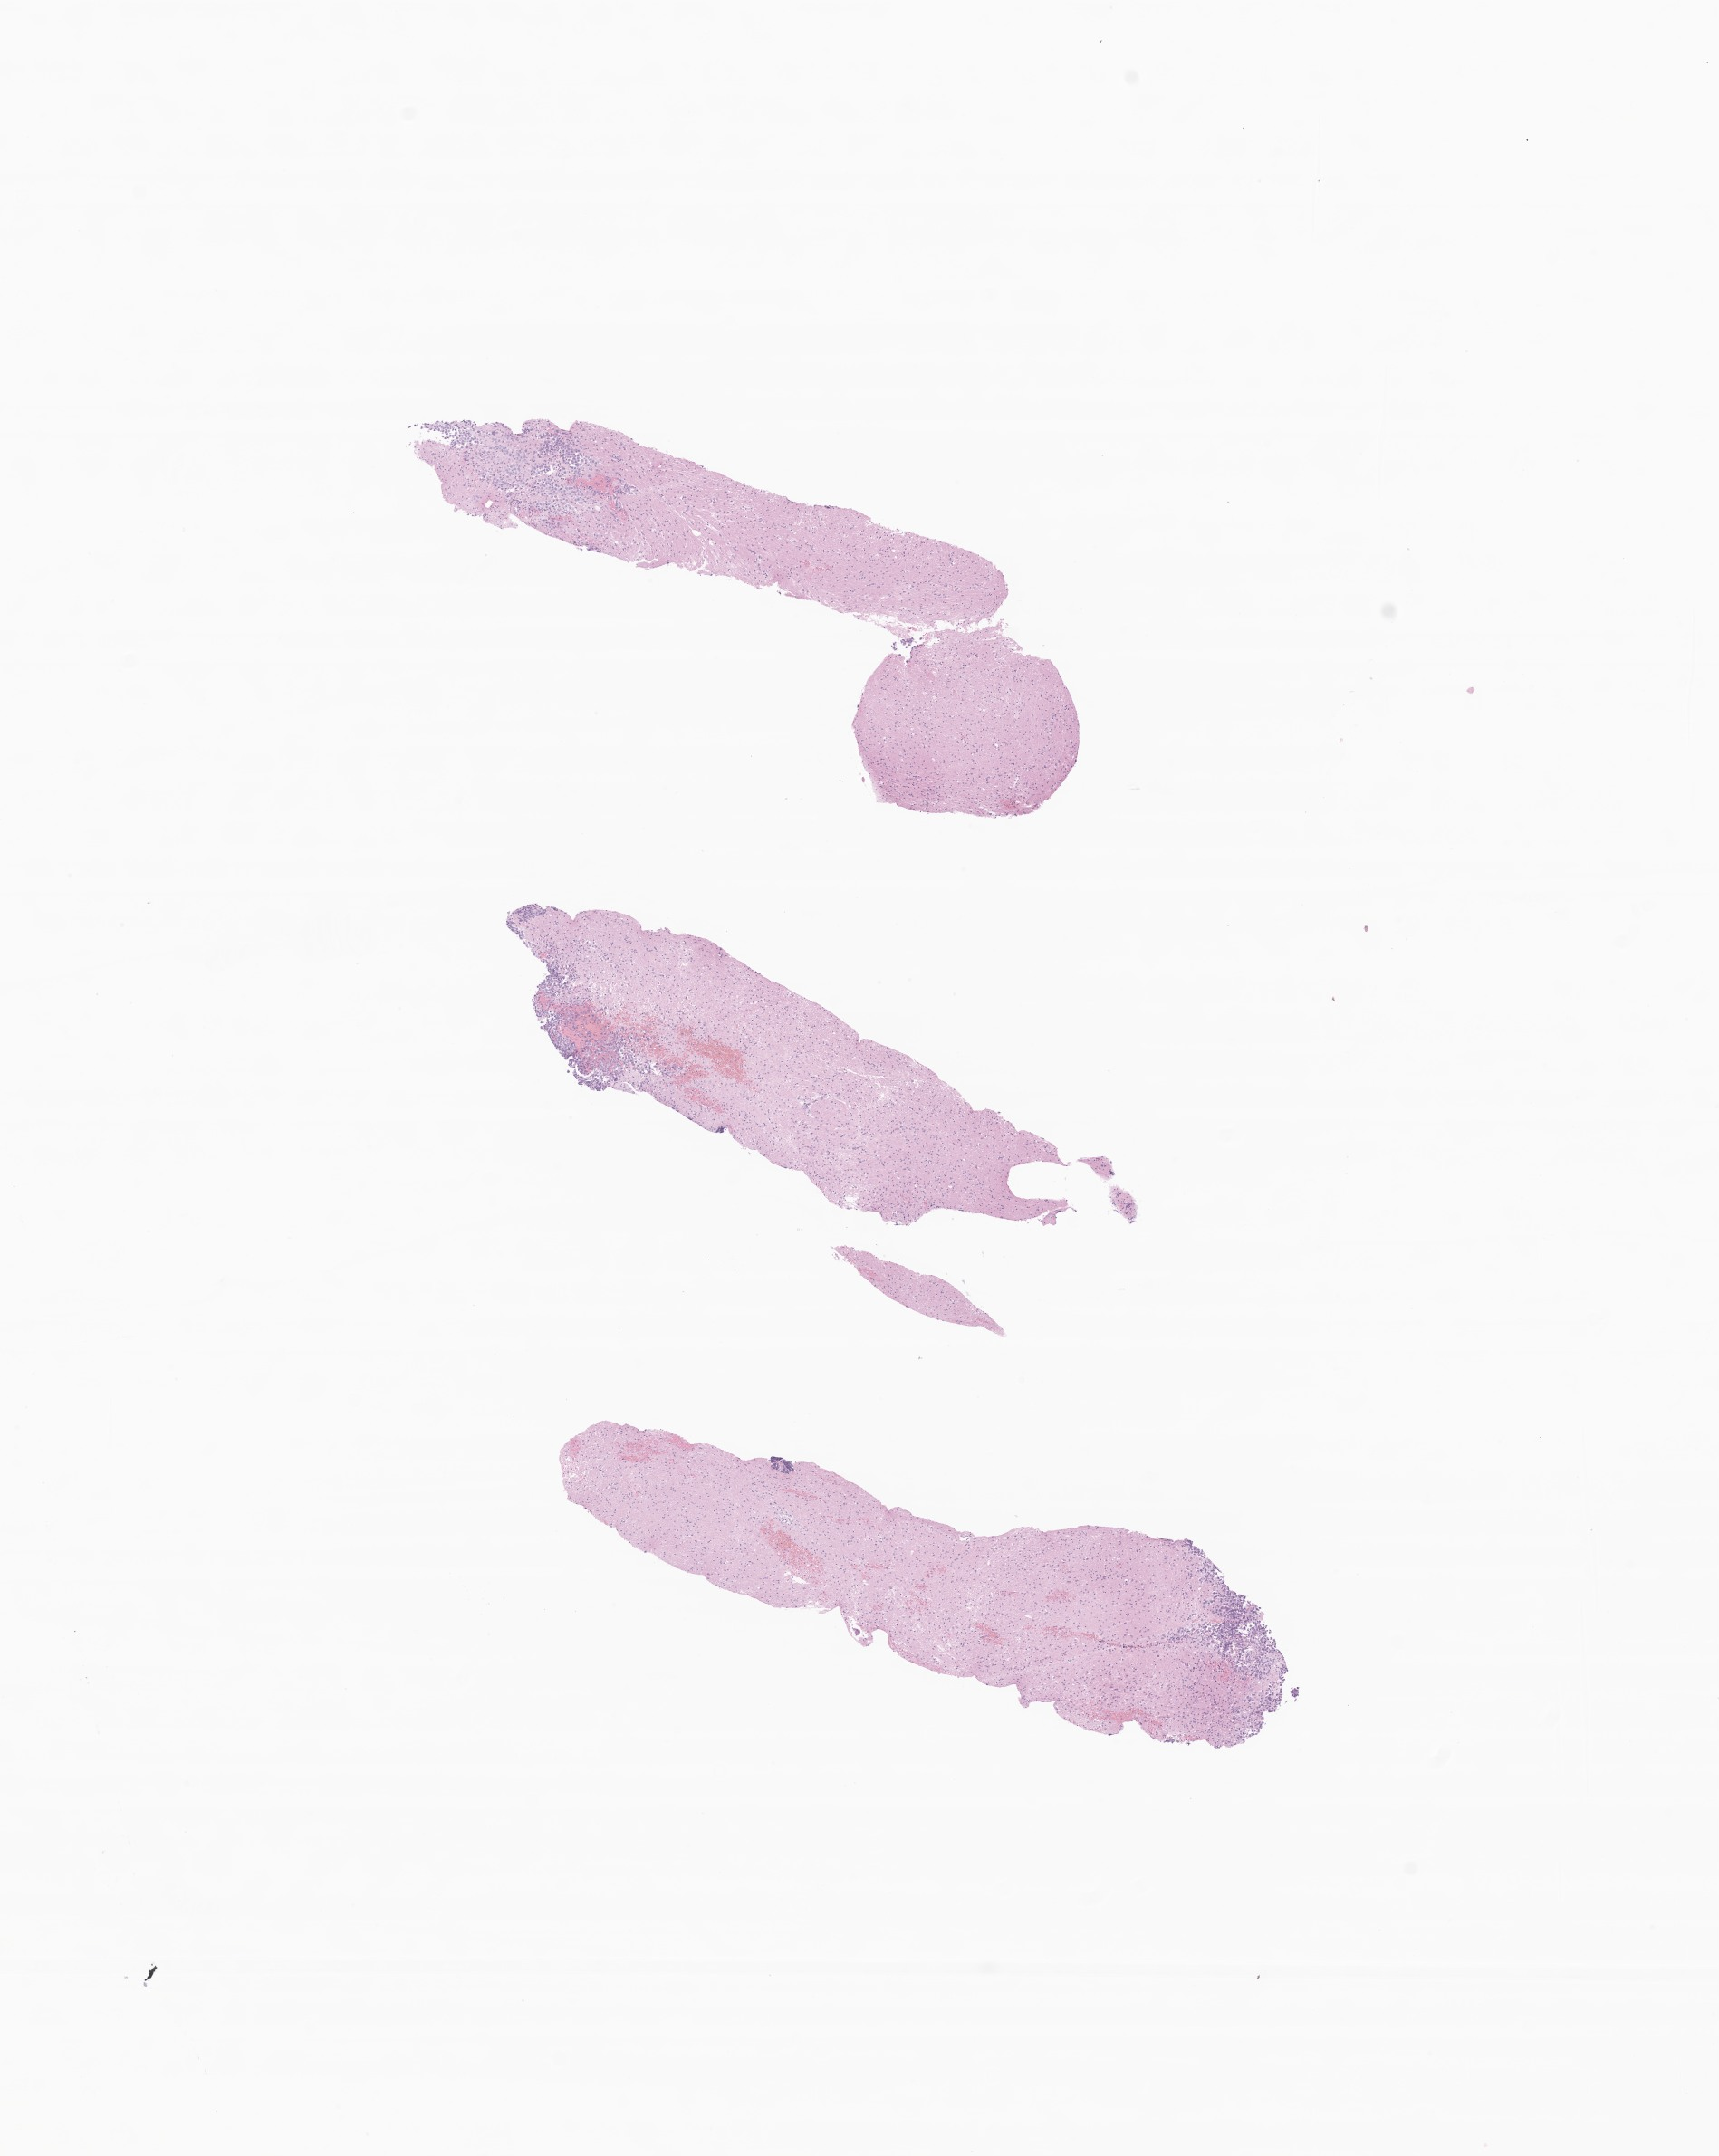
Digitized H&E-stained section of tumor tissue from the brain — whole scanned area (about 8.0 x 10.0 mm) shown as a low-resolution overview, FFPE section. Male patient, age 234 months (19 years 6 months).
Diagnosis: Germinoma.